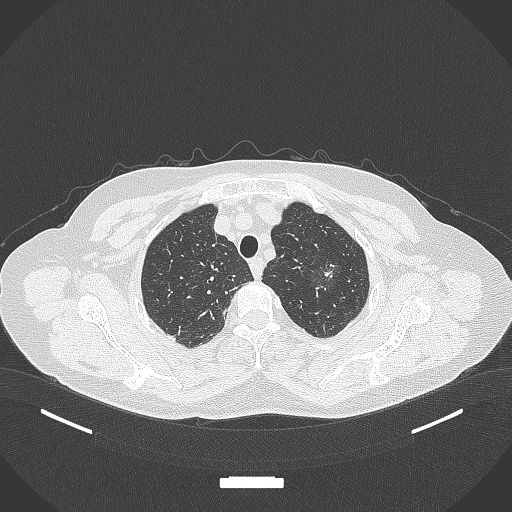
Chest CT, one axial slice. Slice 304 of 369 in the series (ordered by position). Reconstruction kernel B70f. 120 kVp. Lung window (W 1500 / L -600 HU). 512 × 512 image matrix. Patient: female, 64 years. From the clinical record (not read from this slice): clinical TNM (as recorded): T1c N0 M0; histopathological grade: G1.
Annotated regions visible in this slice (rectangle marked by the reading radiologist):
- lung tumour (recorded histology: adenocarcinoma): bounding box (x1, y1, x2, y2) in pixels: (310, 260, 345, 293)